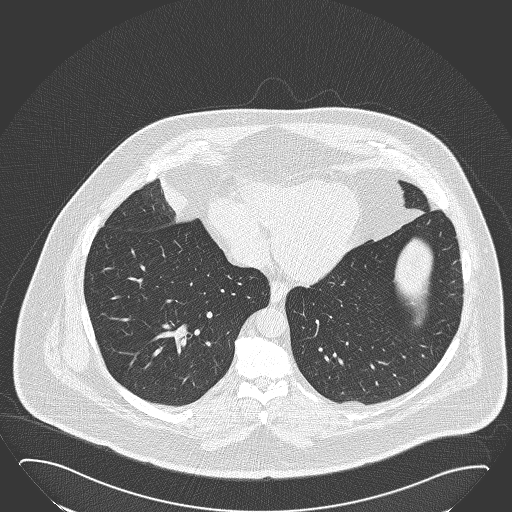
Low-dose screening chest CT, one axial slice. Slice 56 of 168 in the series (ordered by position). Reconstruction kernel B50f. Lung window (W 1500 / L -600 HU). 512 × 512 image matrix.
Structures marked on this image (outlined manually by an expert reader):
- lesion 1 (tumor, hilum of right lung): bounding box [x1, y1, x2, y2] px = [160, 180, 189, 214]